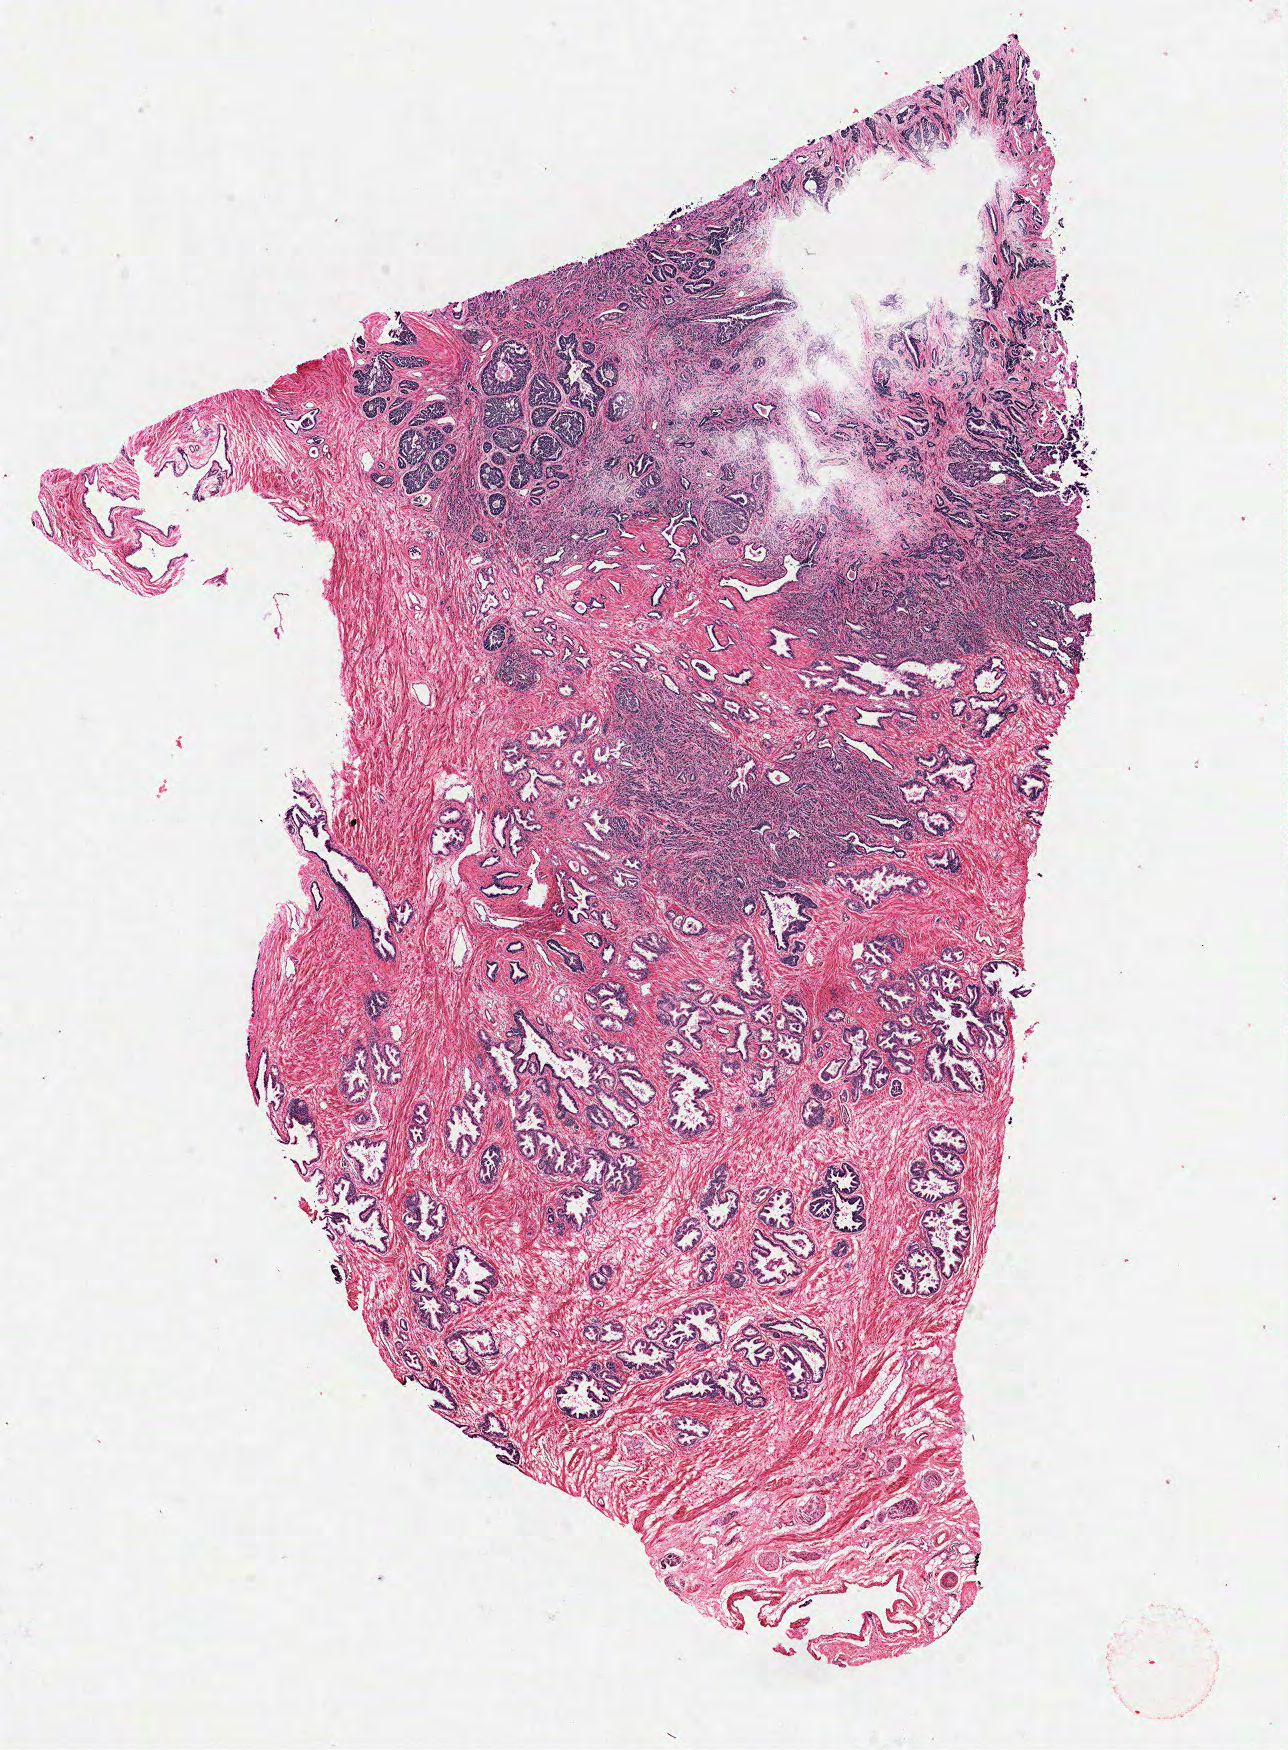
H&E-stained whole-slide image — a low-resolution overview of the entire scanned area, about 10.4 x 14.1 mm; formalin-fixed paraffin-embedded (FFPE) diagnostic section; sample: primary tumour, prostate. Male, age 62 years at initial diagnosis. Gleason score: 9 (4+5).
Laterality: bilateral. Pathologic diagnosis: Acinar cell carcinoma (prostate gland).